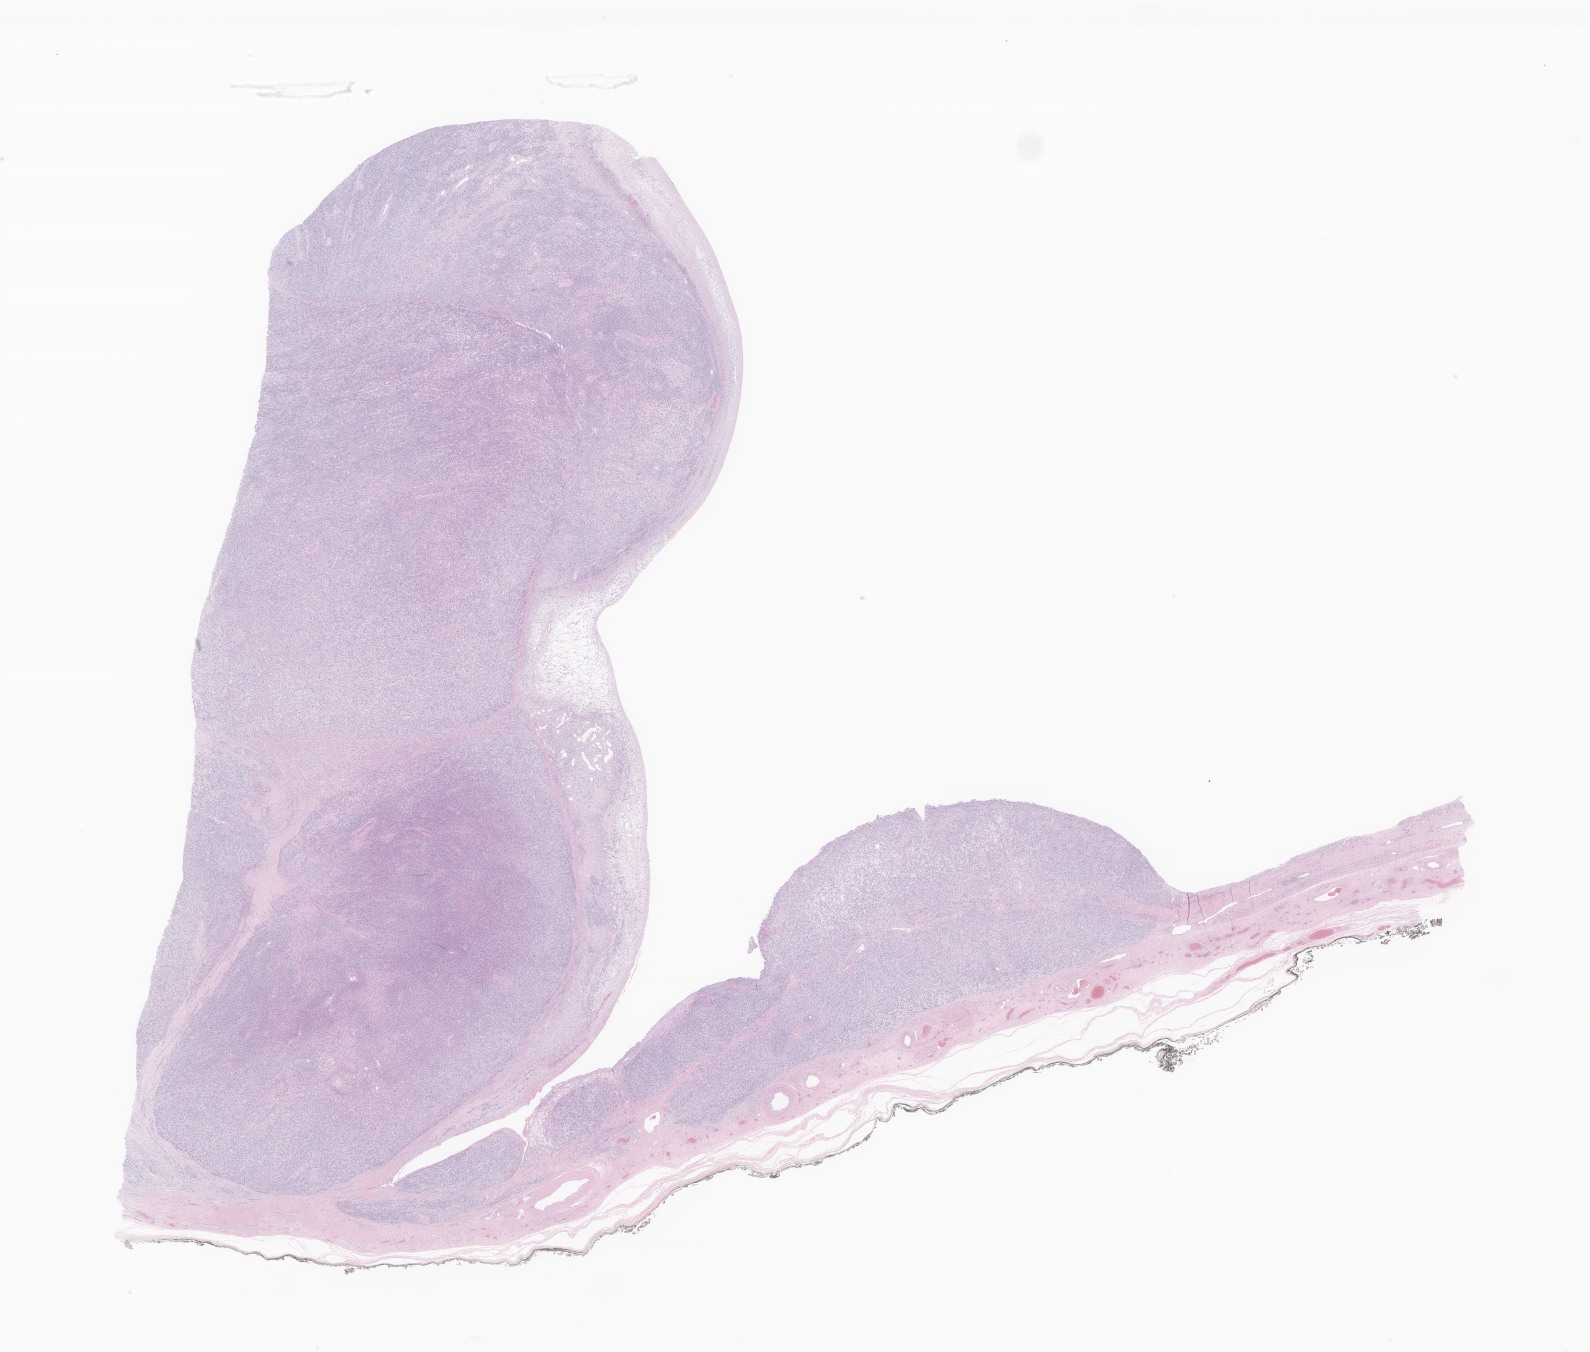
Haematoxylin and eosin whole-slide image of tumor tissue from the testis, whole scanned area (about 26.8 x 22.8 mm) shown as a low-resolution overview, formalin-fixed paraffin-embedded section. Patient: male, age 233 months (19 years 5 months).
• diagnosis (ICD-O-3 morphology term): Rhabdomyosarcoma, NOS